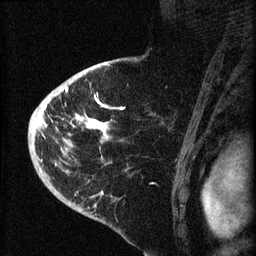
Breast MRI (dynamic contrast-enhanced), one sagittal slice. Dynamic contrast-enhanced series, image 2 of 4 at this slice position (ordered by acquisition). 1.5 T. TE 4.2 ms, TR 8.2 ms. 256 × 256 image matrix. Female patient, age 71 years.
Outlined on this slice (semi-automatically segmented with operator editing):
- analysis volume of interest (the breast-tissue region the enhancement analysis was run in; not a lesion): bounding box (x1, y1, x2, y2) in pixels: (35, 75, 133, 190)
- tumour enhancement mask (voxels above the 70 % enhancement threshold inside the analysis volume of interest): (35, 86, 125, 162)